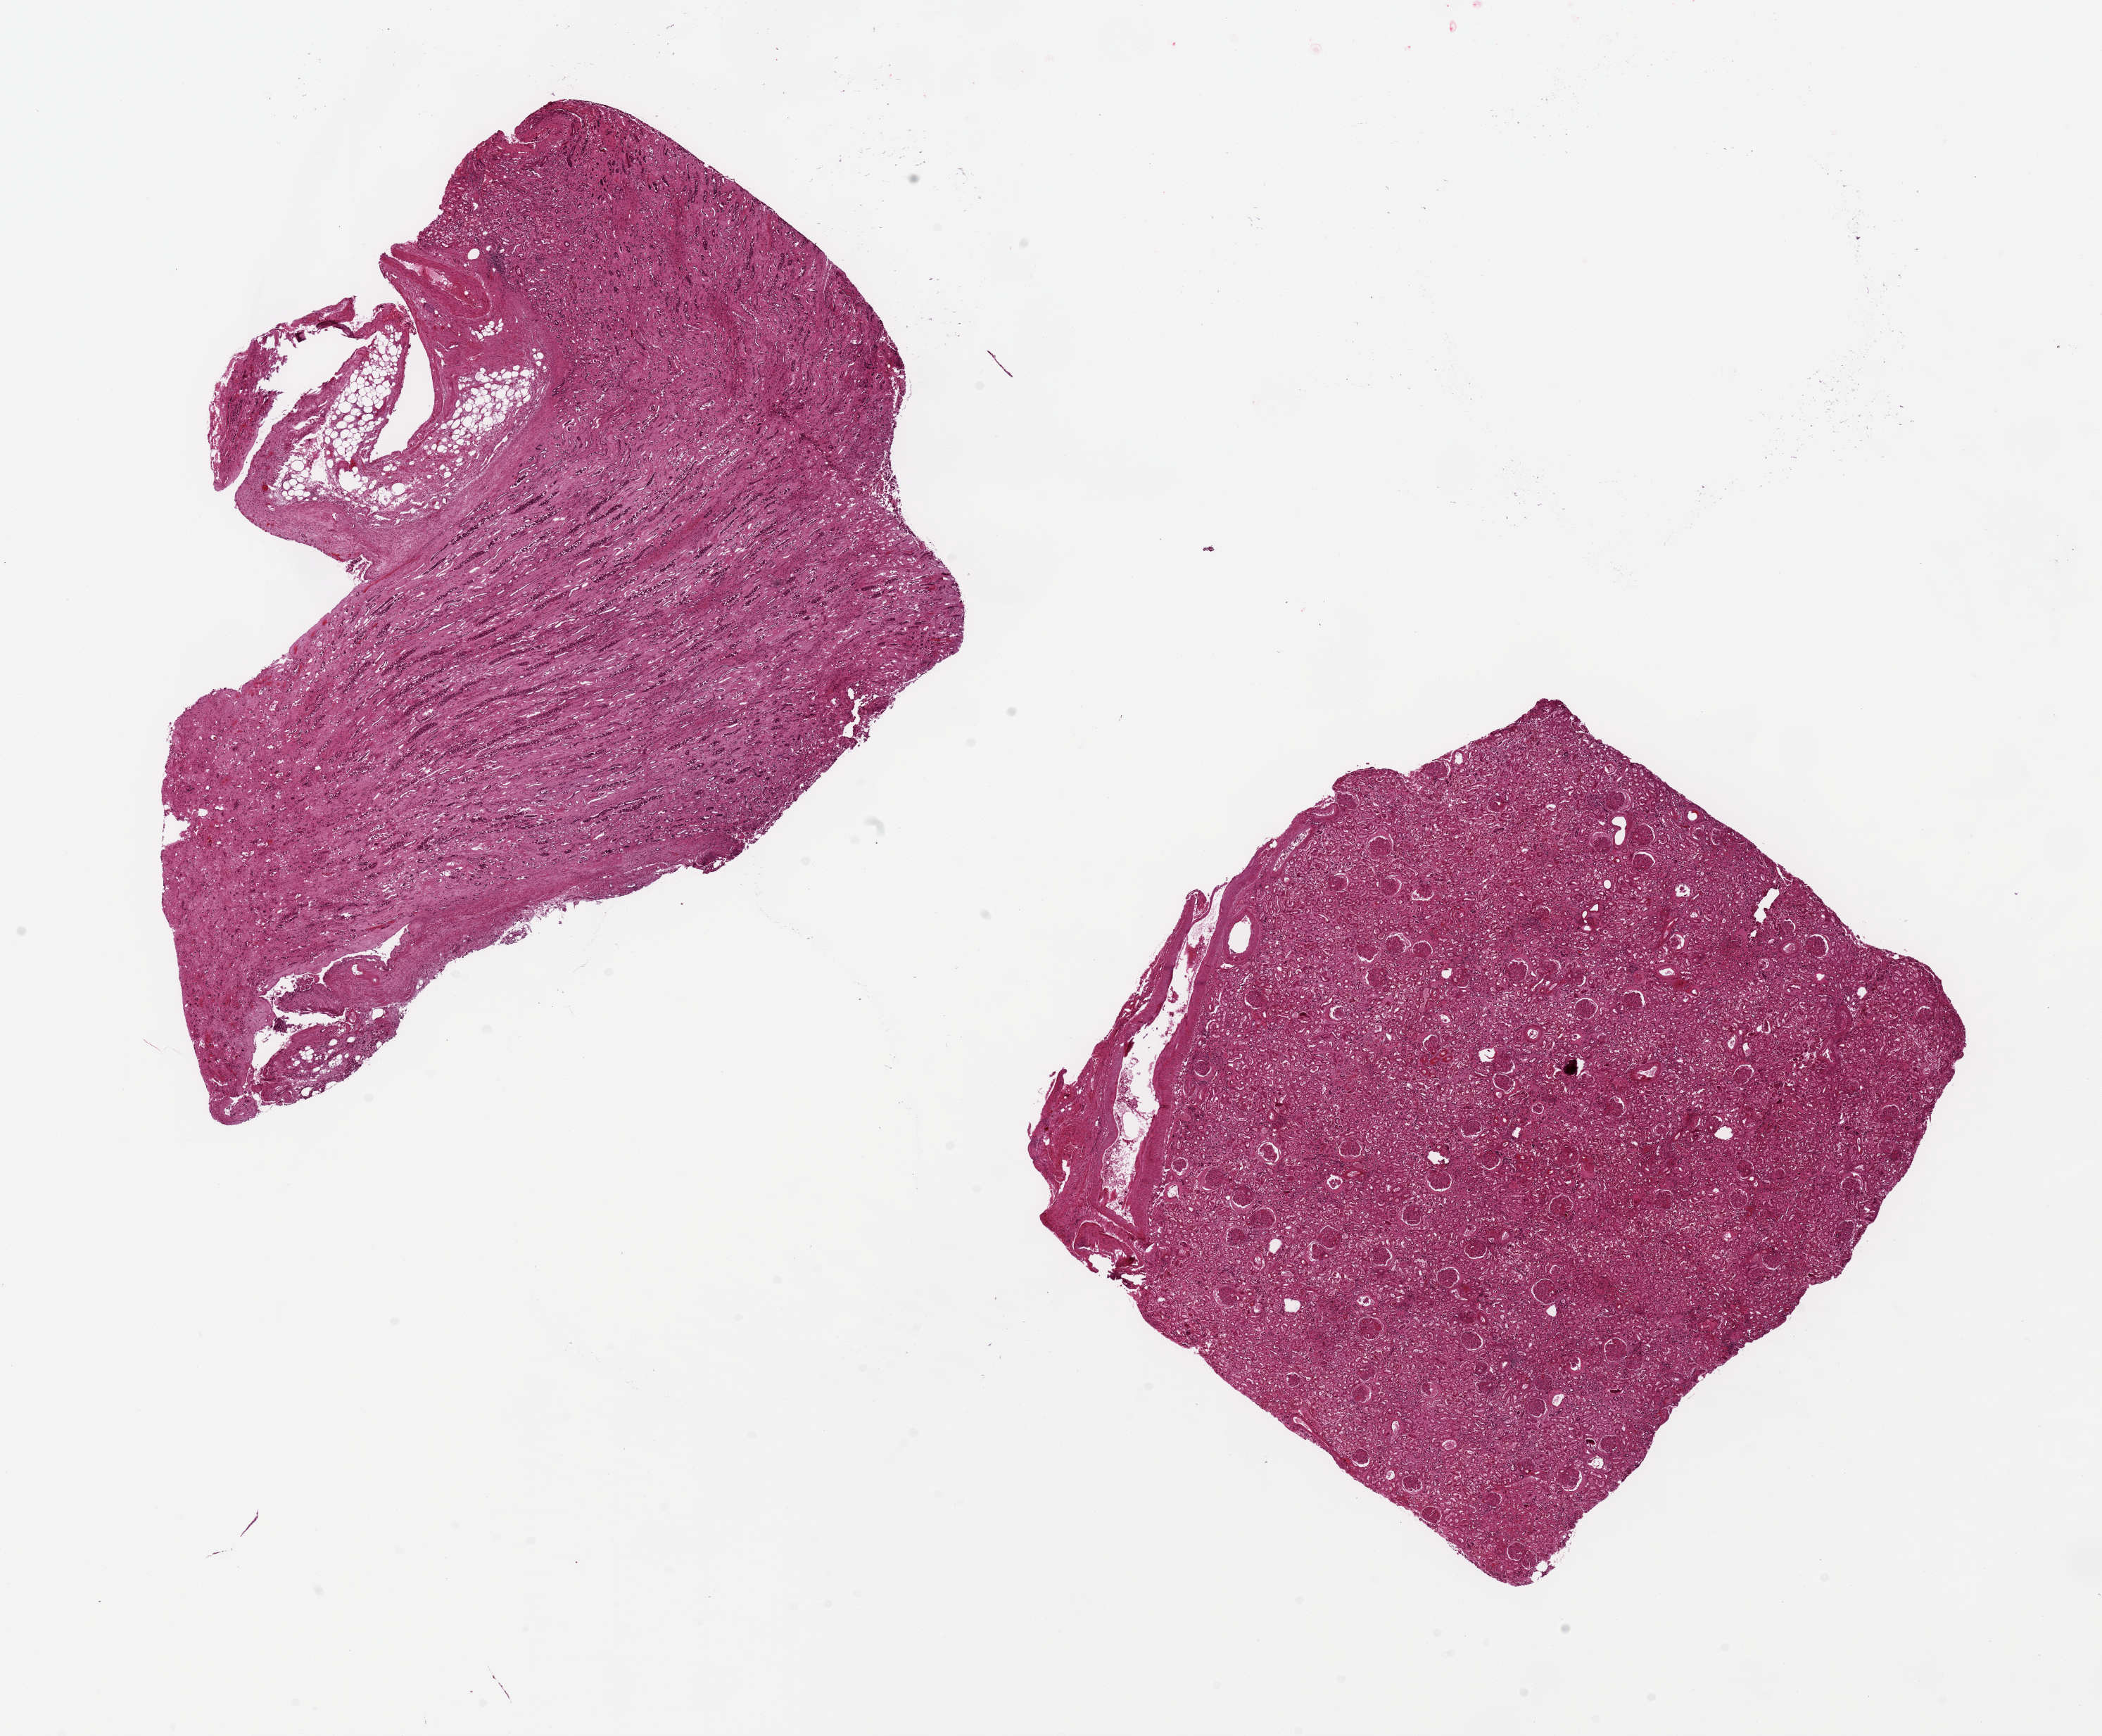
Digitized H&E-stained section — low-resolution overview of the scanned area, about 23.6 x 19.5 mm (acquisition: 20x scan). PAXgene-fixed paraffin-embedded (PFPE) section. Section of renal medulla (target tissue). Tissue donor sample. Donor sex: male.
Pathologist's review note for this sample: 2 ~8x7mm pieces. One with glomeruli, one ???pure??? medulla.